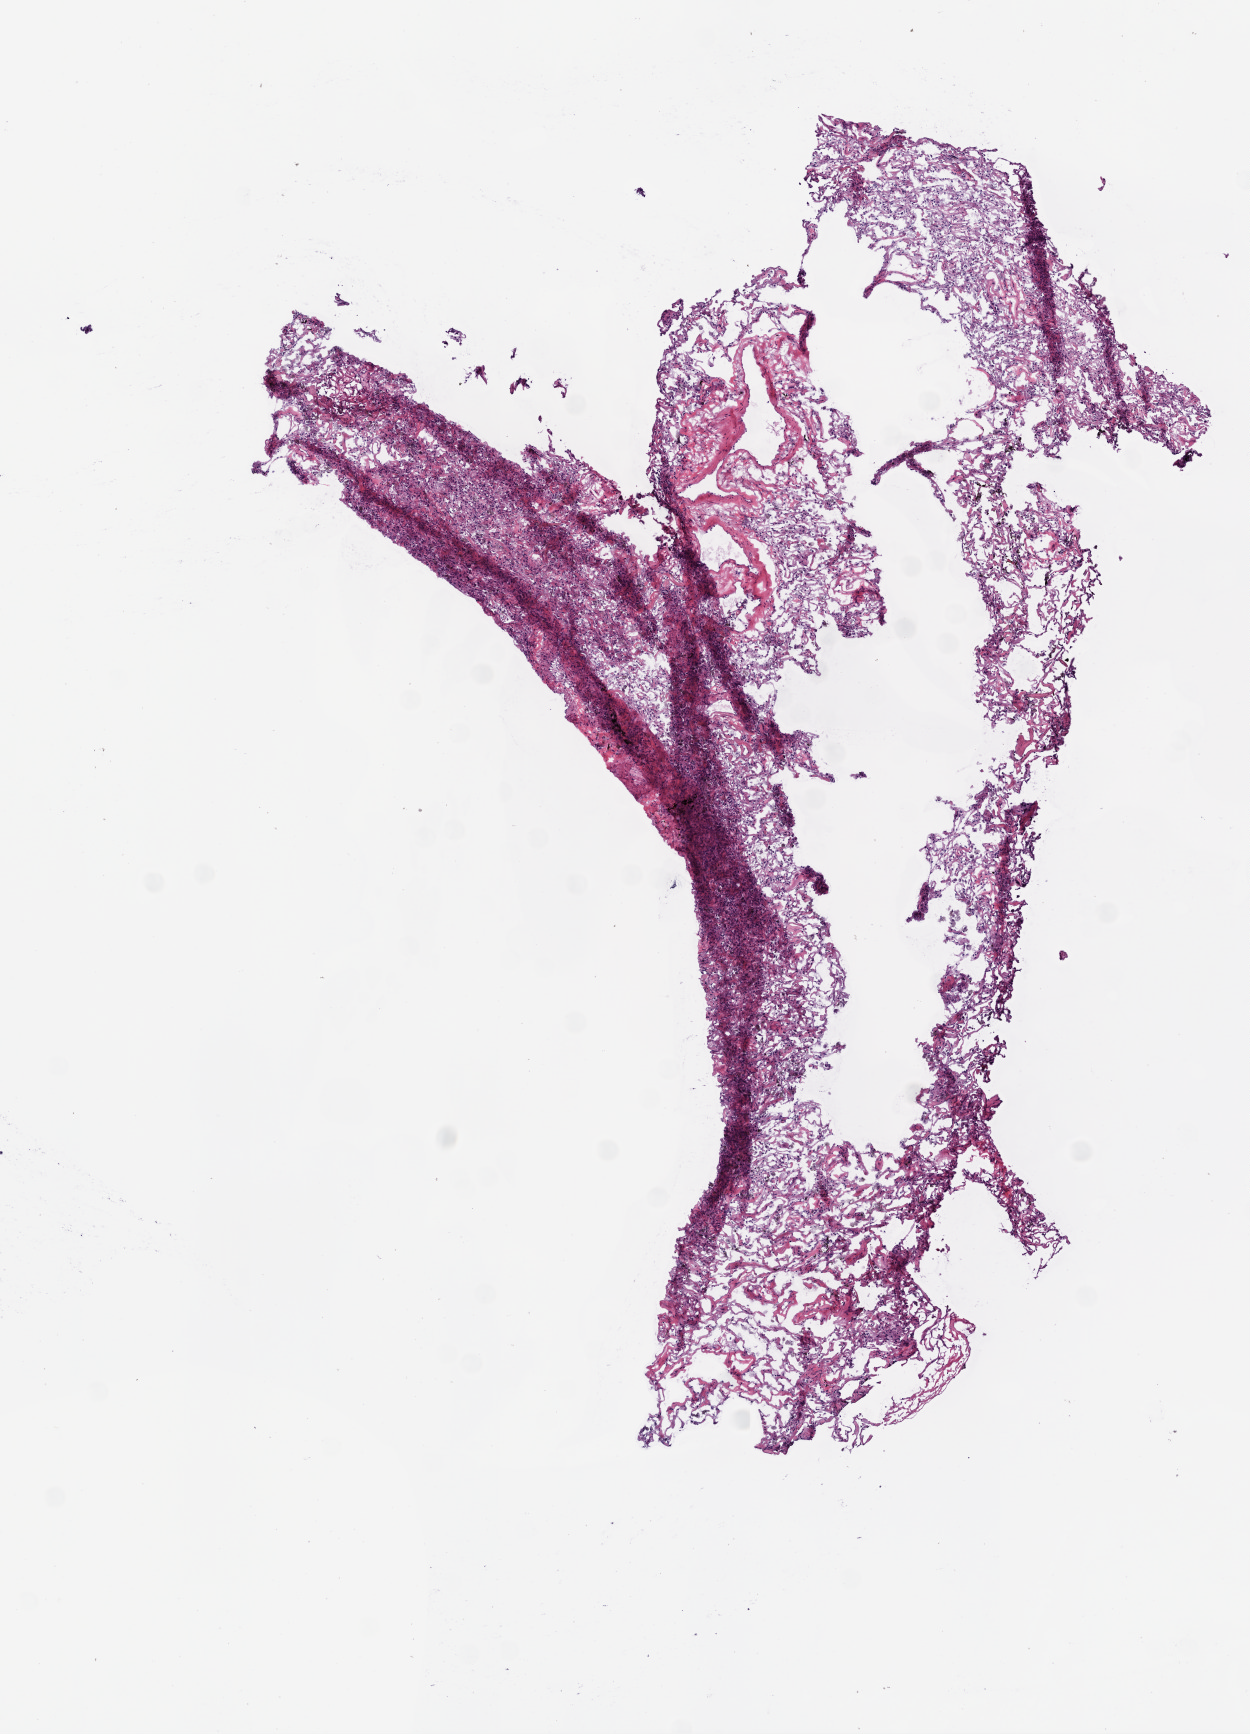
Digitized H&E-stained tissue section (whole slide) — whole scanned area (about 5.0 x 7.0 mm) shown as a low-resolution overview. Frozen section from the bottom of the tissue portion. Lung, solid tissue normal (non-tumour tissue) sample. Patient: female, age at initial diagnosis 77 years.
This section: solid tissue normal sample (biorepository sample class). Patient diagnosis: Squamous cell carcinoma, NOS (lower lobe, lung).